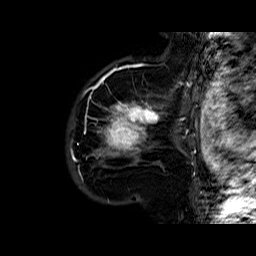
Breast MRI (dynamic contrast-enhanced), one sagittal slice. Position 46 of 60 along the scan axis. Dynamic contrast-enhanced series, time point 2 of 6 at this slice position (early post-contrast). 1.5 T. TE 6.4 ms, TR 32.8 ms. 256 × 256 image matrix, field of view 200 × 200 mm. Female patient. From the clinical record (not read from this slice): setting: breast cancer imaged before/during neoadjuvant chemotherapy; receptor status: HR-positive, HER2-negative.
Outlined on this slice (semi-automatic segmentation, software-assisted and operator-edited):
- analysis volume of interest (the breast-tissue region the enhancement analysis was run in; not a lesion): bounding box (x1, y1, x2, y2) in pixels: (87, 77, 163, 177)
- tumour enhancement mask (voxels above the 100 % enhancement threshold inside the analysis volume of interest): (96, 78, 160, 156)